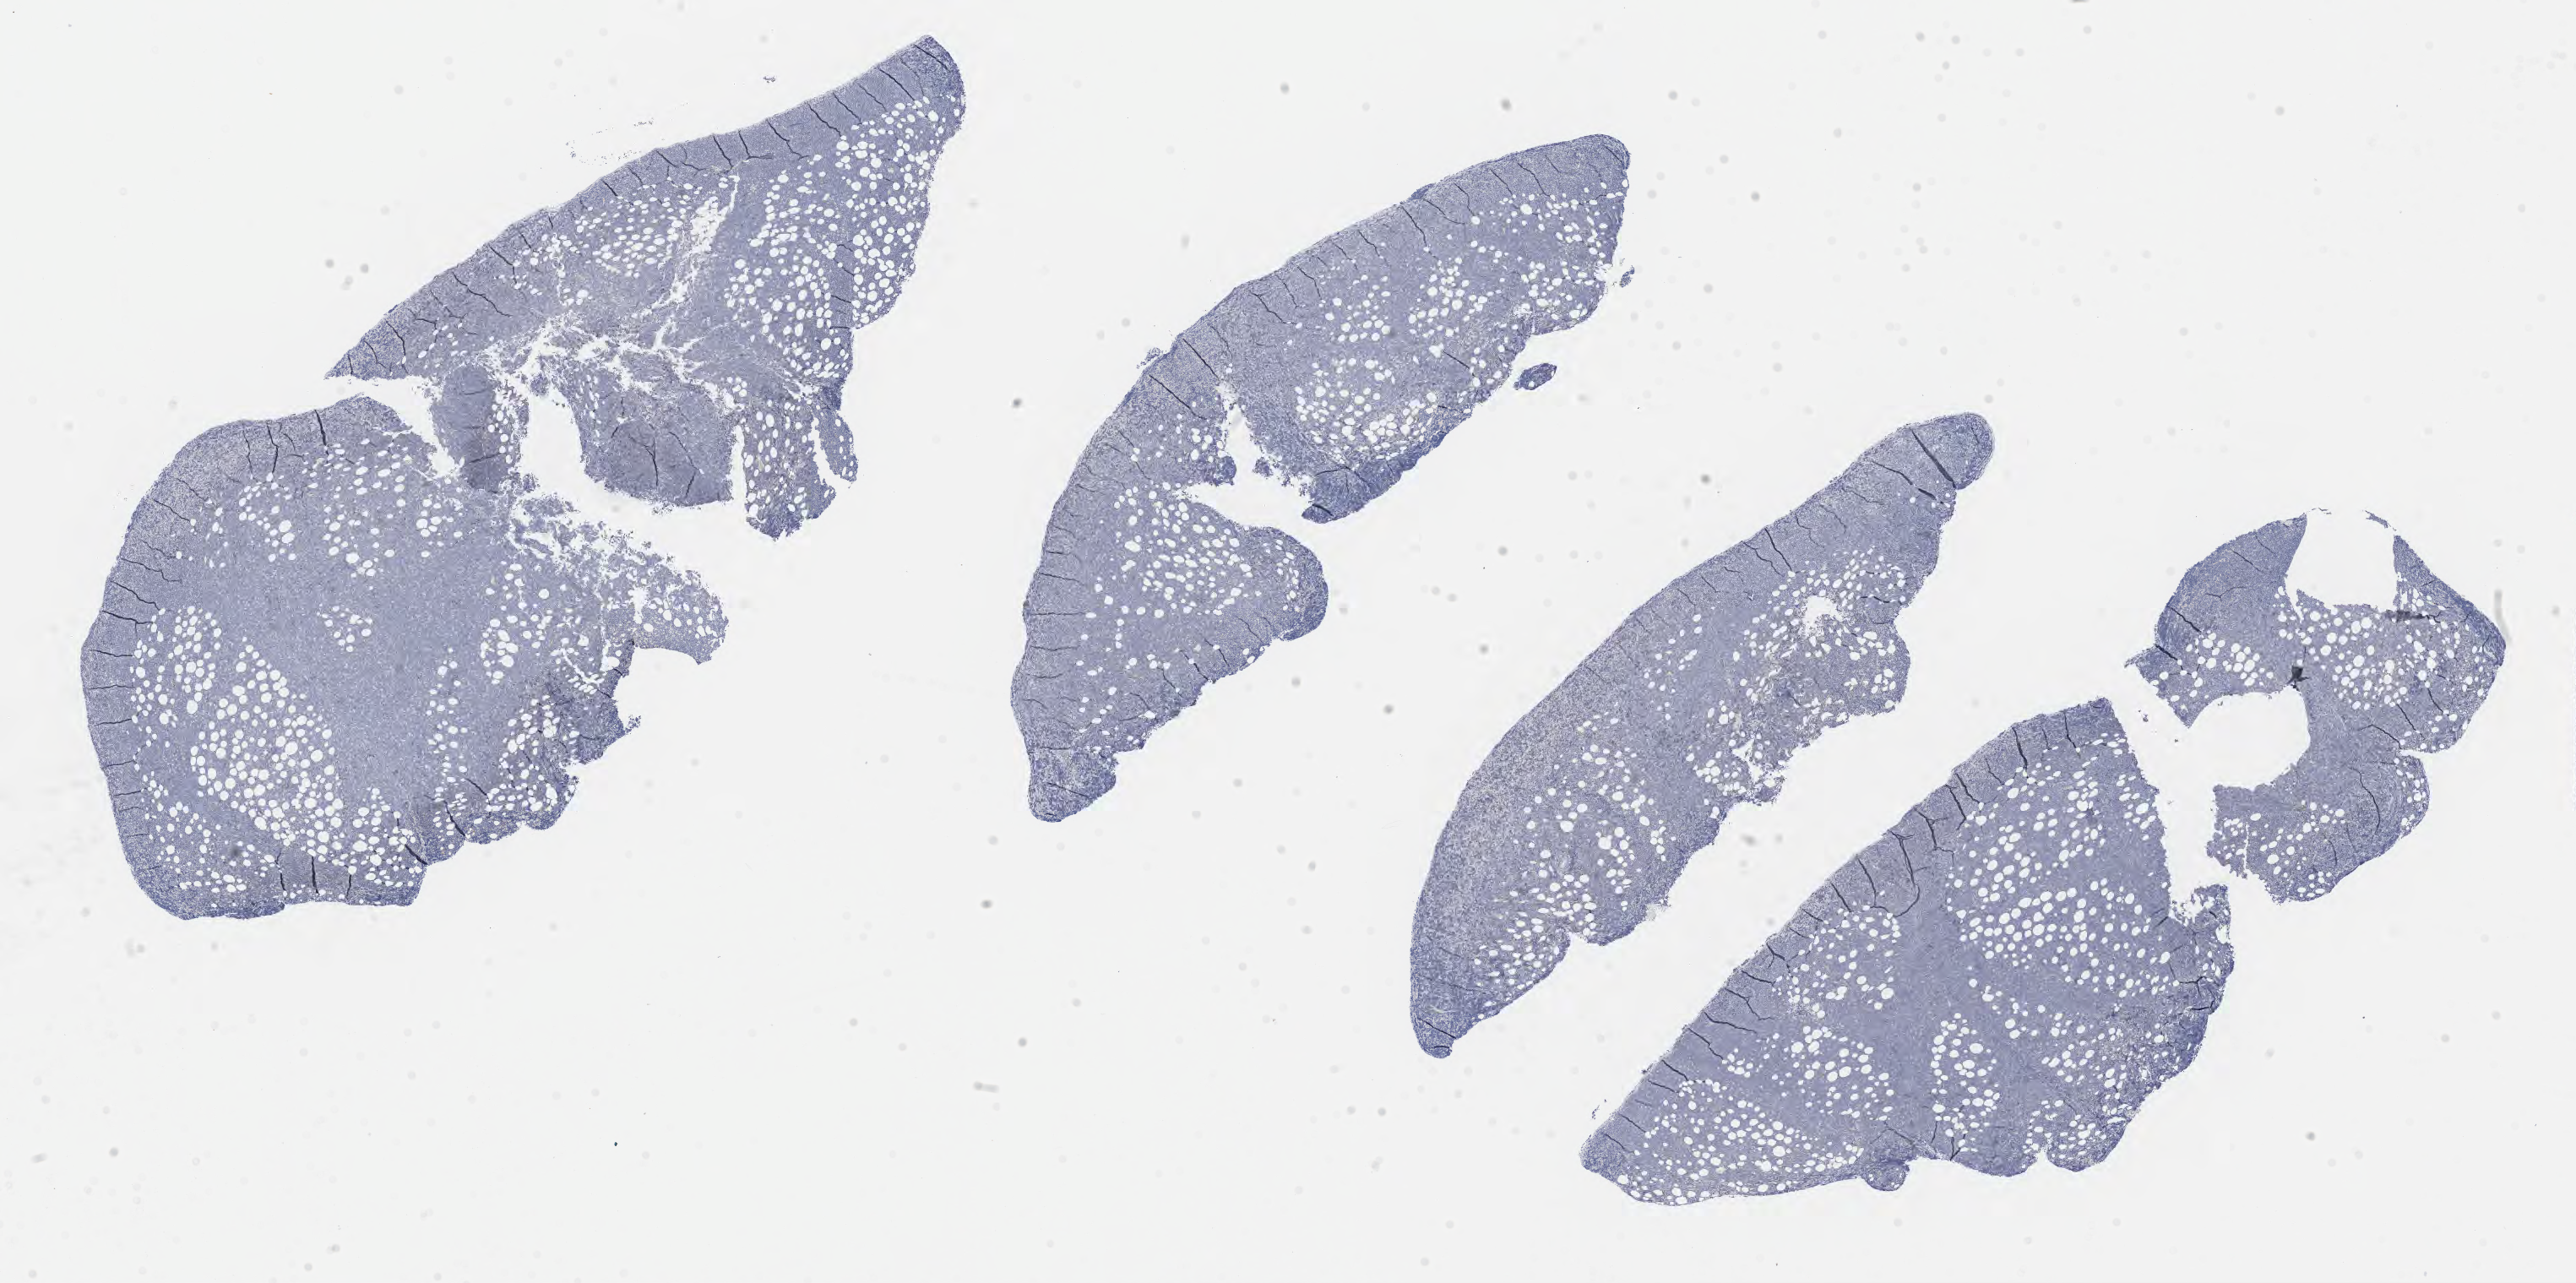
IHC for BCL2, whole-slide image, a low-resolution overview of the entire scanned area, about 24.7 x 12.3 mm; specimen: tumor tissue. Patient male; age 52 years.
Diagnosis: Diffuse large B-cell lymphoma, NOS.